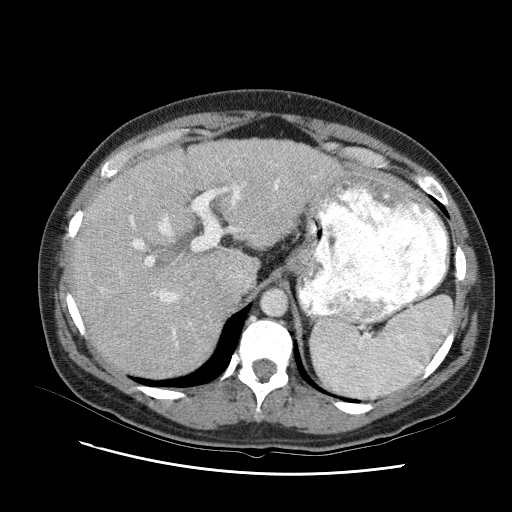
Contrast-enhanced abdominal CT (liver protocol), one axial slice; position 68 of 95 along the scan axis; reconstruction kernel STANDARD; 120 kVp; one of 2 acquisitions stored at this slice position; soft-tissue window (W 400 / L 40 HU); 512 × 512 image matrix, field of view 360 × 360 mm. Case-level facts recorded for this patient, not image findings: diagnosis: hepatocellular carcinoma (patient treated with transarterial chemoembolisation; whether this scan precedes or follows treatment is not stated here); TNM stage (as recorded): Stage-I; Child-Pugh class: B; tumour nodularity: uninodular.
Annotated regions visible in this slice (semi-automatically segmented with operator editing):
- liver parenchyma outside the tumour (the mass and vessels are separate outlines, so this box may not span the whole liver): bounding box (x1, y1, x2, y2) in pixels: (68, 136, 340, 364)
- liver vessels: (88, 159, 318, 327)